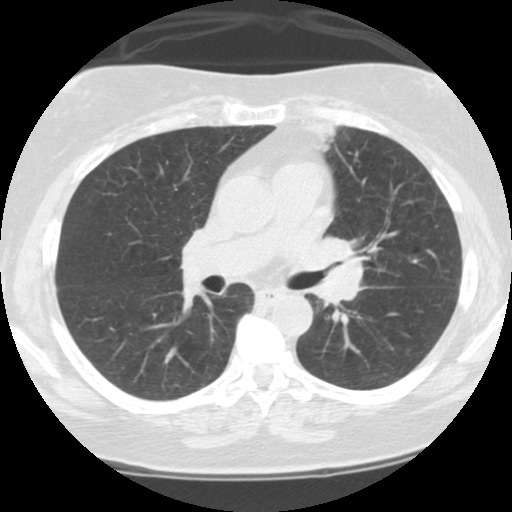
Low-dose screening chest CT, axial slice. Third screening round (two years after baseline). Lung window (W 1500 / L -600 HU). Standard (soft-tissue) reconstruction kernel (STANDARD). Slice 46 of 108 in the series. Female participant, aged 59 years at enrolment. Current smoker at enrolment.
- Expert reader's lesion annotation, bounding box (x1, y1, x2, y2) in pixels: (285, 213, 388, 325).
- No non-calcified nodule or mass ≥4 mm was recorded by the screening reader at this exam.